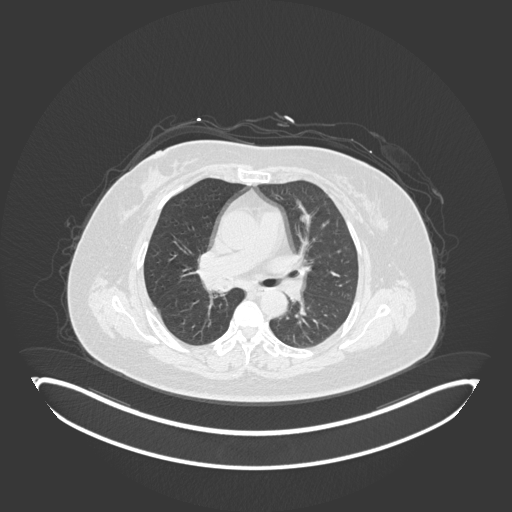
Chest CT, one axial slice. 120 kVp. Lung window (W 1500 / L -600 HU). 1 mm slice thickness. 512 × 512 image matrix, field of view 500 × 500 mm. Patient: female, 60 years. From the clinical record (not read from this slice): clinical TNM (as recorded): T1c N0 M0.
Annotated regions visible in this slice (rectangle marked by the reading radiologist):
- lung tumour (recorded histology: squamous cell carcinoma): bounding box [x1, y1, x2, y2] px = [203, 272, 237, 296]